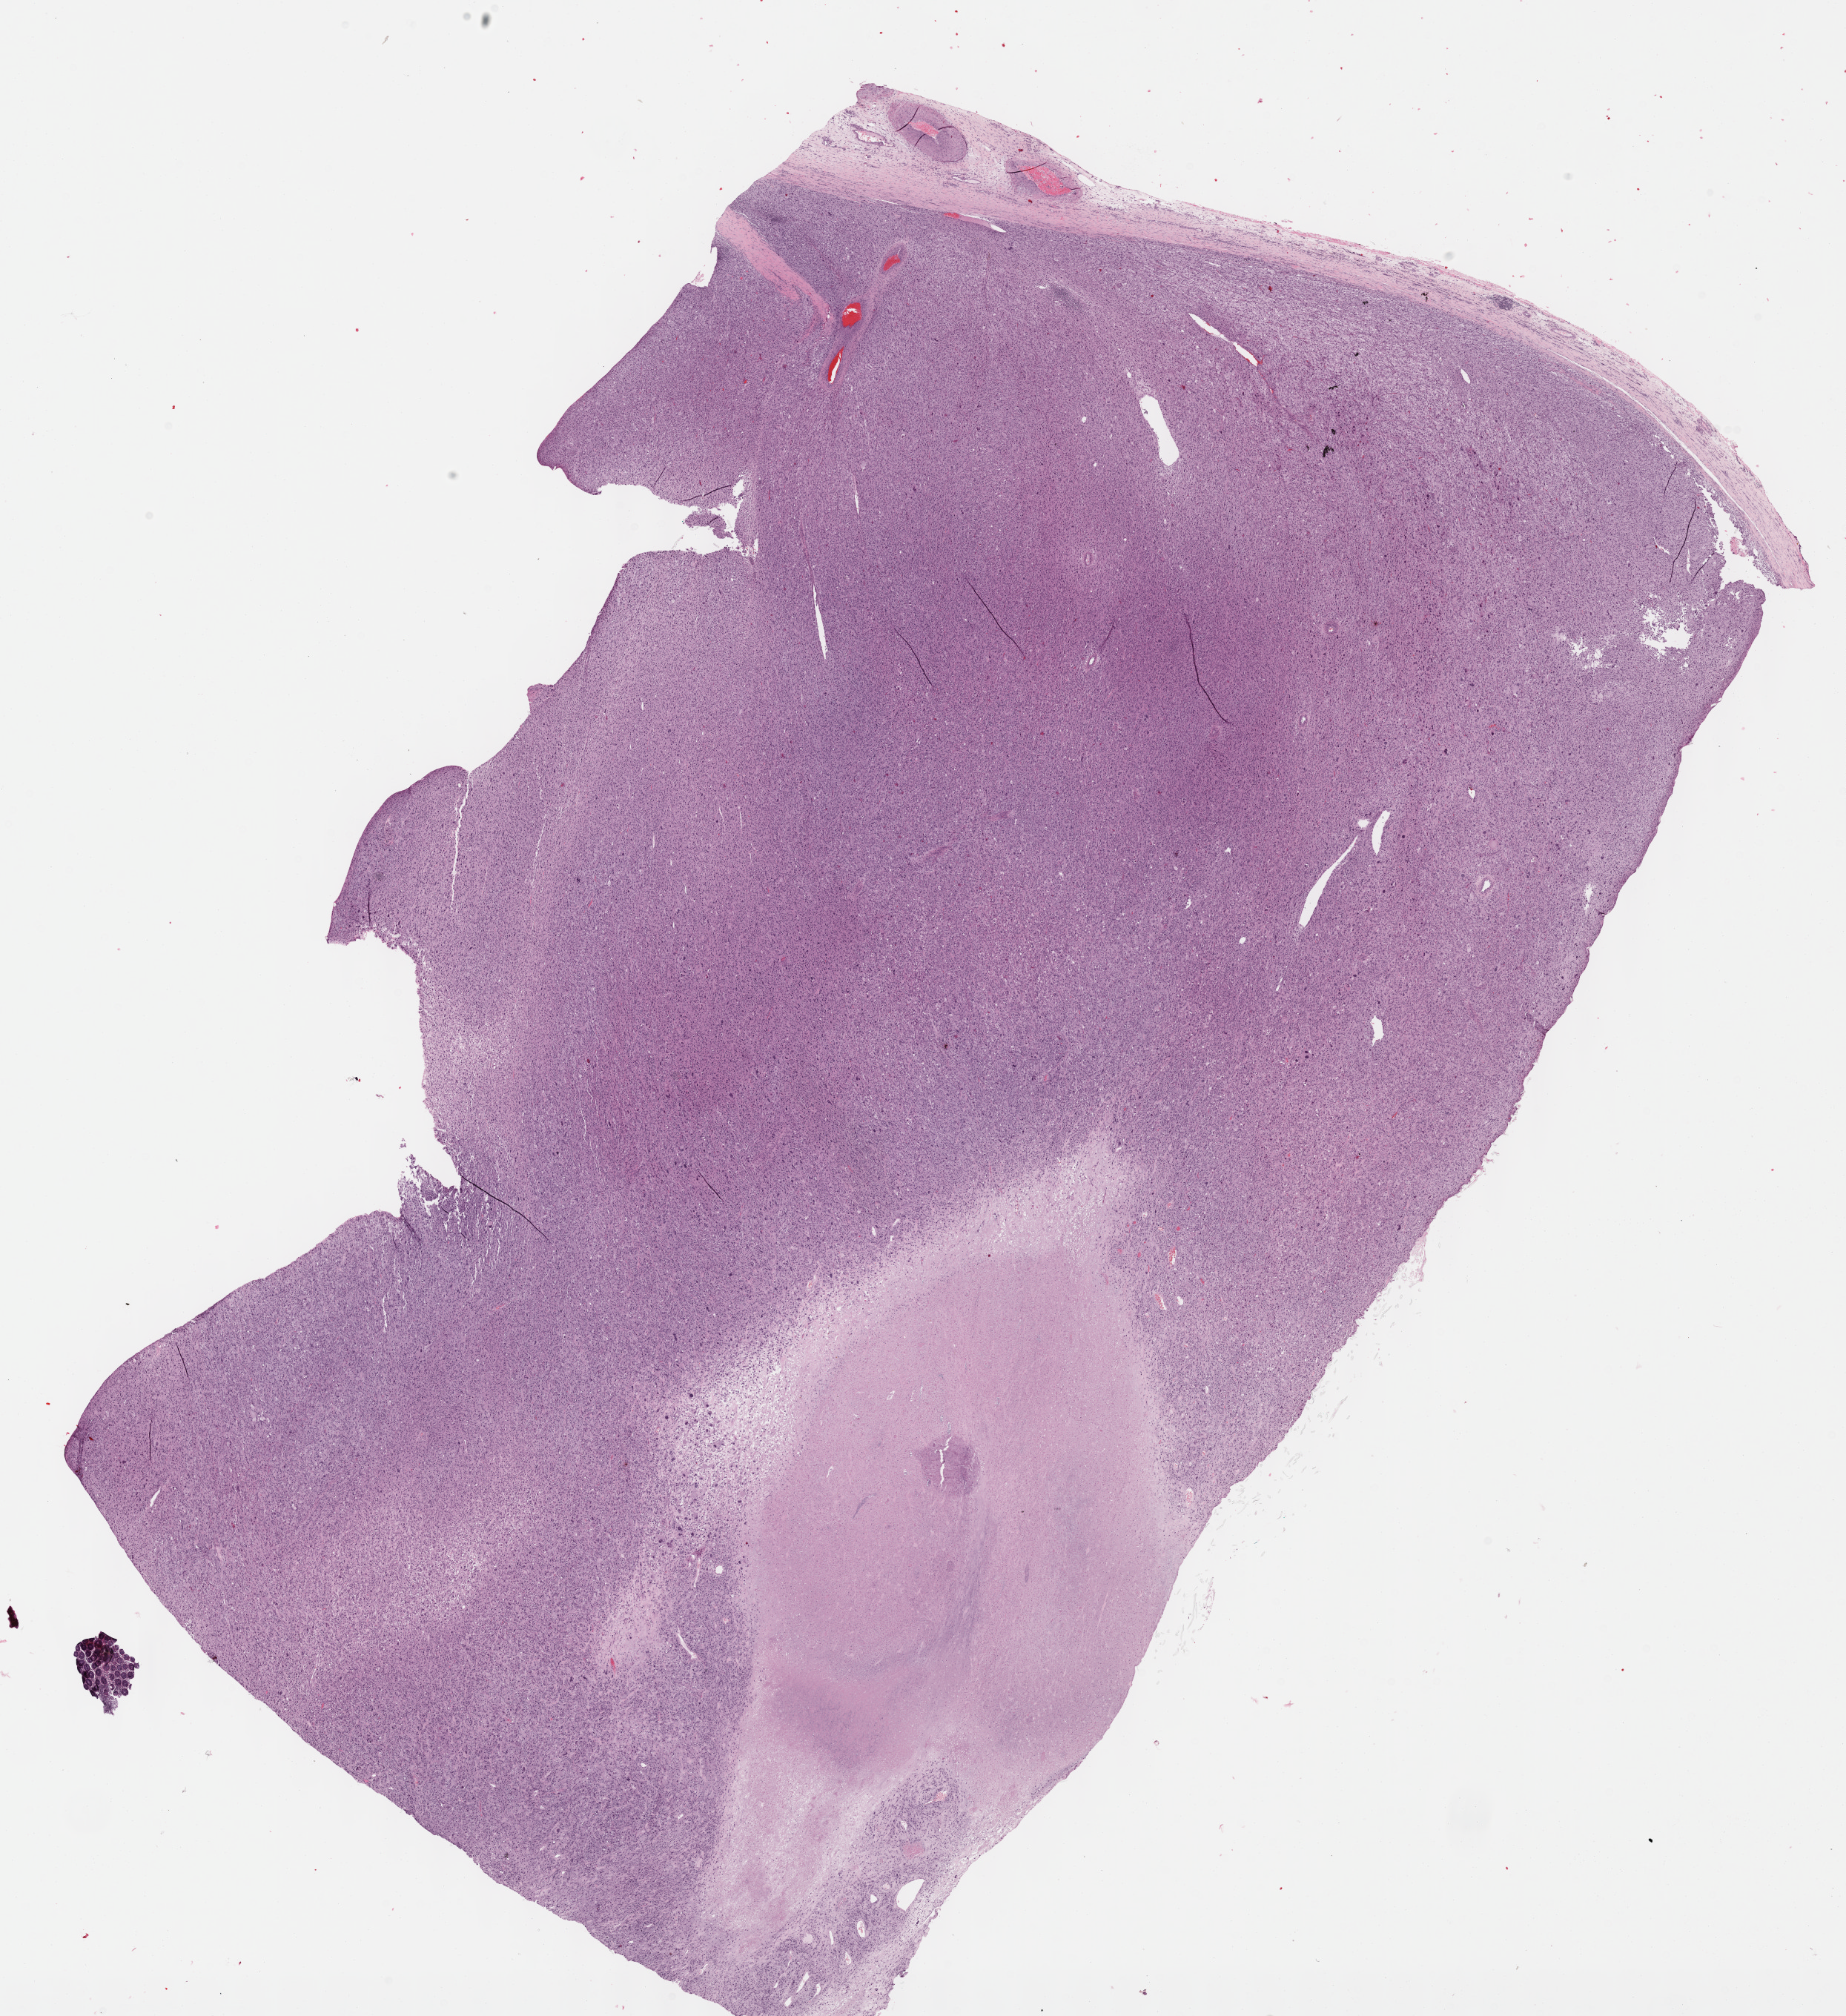
Whole-slide histology image, Hematoxylin and eosin (H&E) stained — whole scanned area (about 20.1 x 22.0 mm, slide scanned at 40x) shown as a low-resolution overview; FFPE section; sample: primary tumour, connective, subcutaneous and other soft tissues. Male patient; age at initial diagnosis 60 years.
Pathologic diagnosis: Undifferentiated sarcoma (connective, subcutaneous and other soft tissues of lower limb and hip).